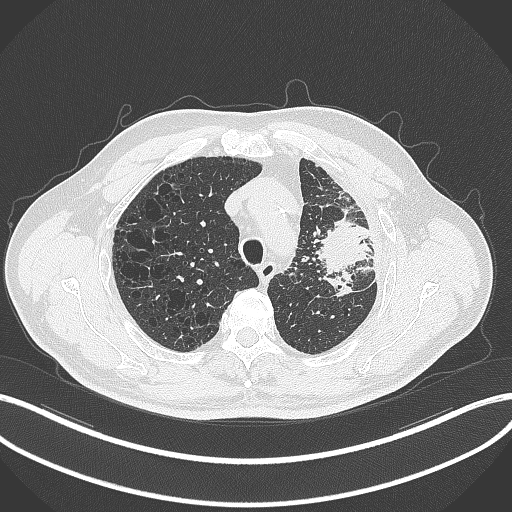
Chest CT, one axial slice. Position 251 of 297 along the scan axis. 120 kVp. Lung window (W 1500 / L -600 HU). 1 mm slice thickness. 512 × 512 image matrix, field of view 400 × 400 mm. Patient: male, 68 years. From the clinical record (not read from this slice): clinical TNM (as recorded): T3 N3 M1.
Structures marked on this image (rectangle marked by the reading radiologist):
- lung tumour (recorded histology: adenocarcinoma): box from (x=314, y=209) to (x=369, y=282) px